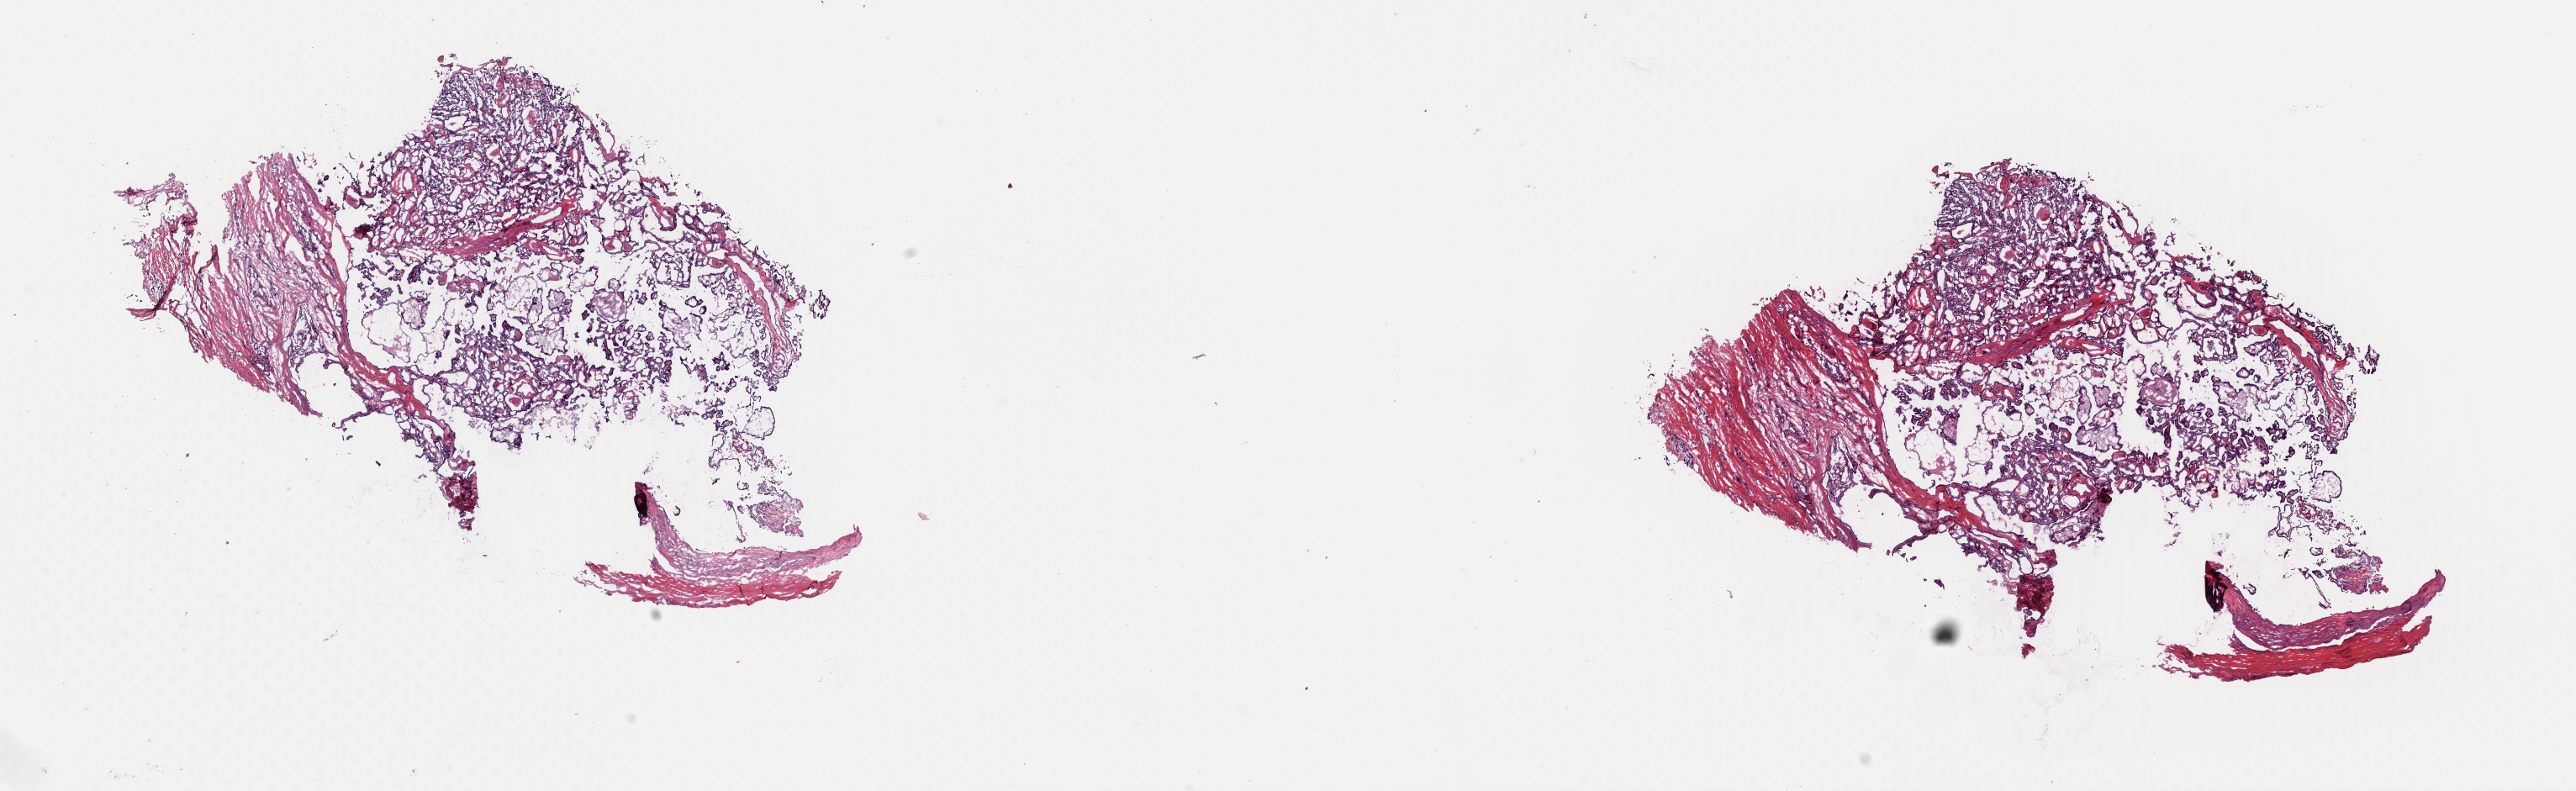
Digitized H&E-stained tissue section (whole slide) — low-resolution overview of the scanned area, about 24.2 x 7.4 mm. Frozen section. Thyroid, primary tumour sample. Patient: female, age at initial diagnosis 45 years. Composition of this section per pathologist review: tumour cells 90%, tumour nuclei 95%, normal cells 0%, stromal cells 10%, necrosis 0%. Inflammatory infiltration, as recorded: lymphocyte infiltration 0%, monocyte infiltration 0%, neutrophil infiltration 0%.
Lymph nodes positive (case pathology): 2 of 4 examined. Histologic diagnosis: Papillary adenocarcinoma, NOS (thyroid gland). Laterality: left. AJCC pathologic stage: III (7th edition).